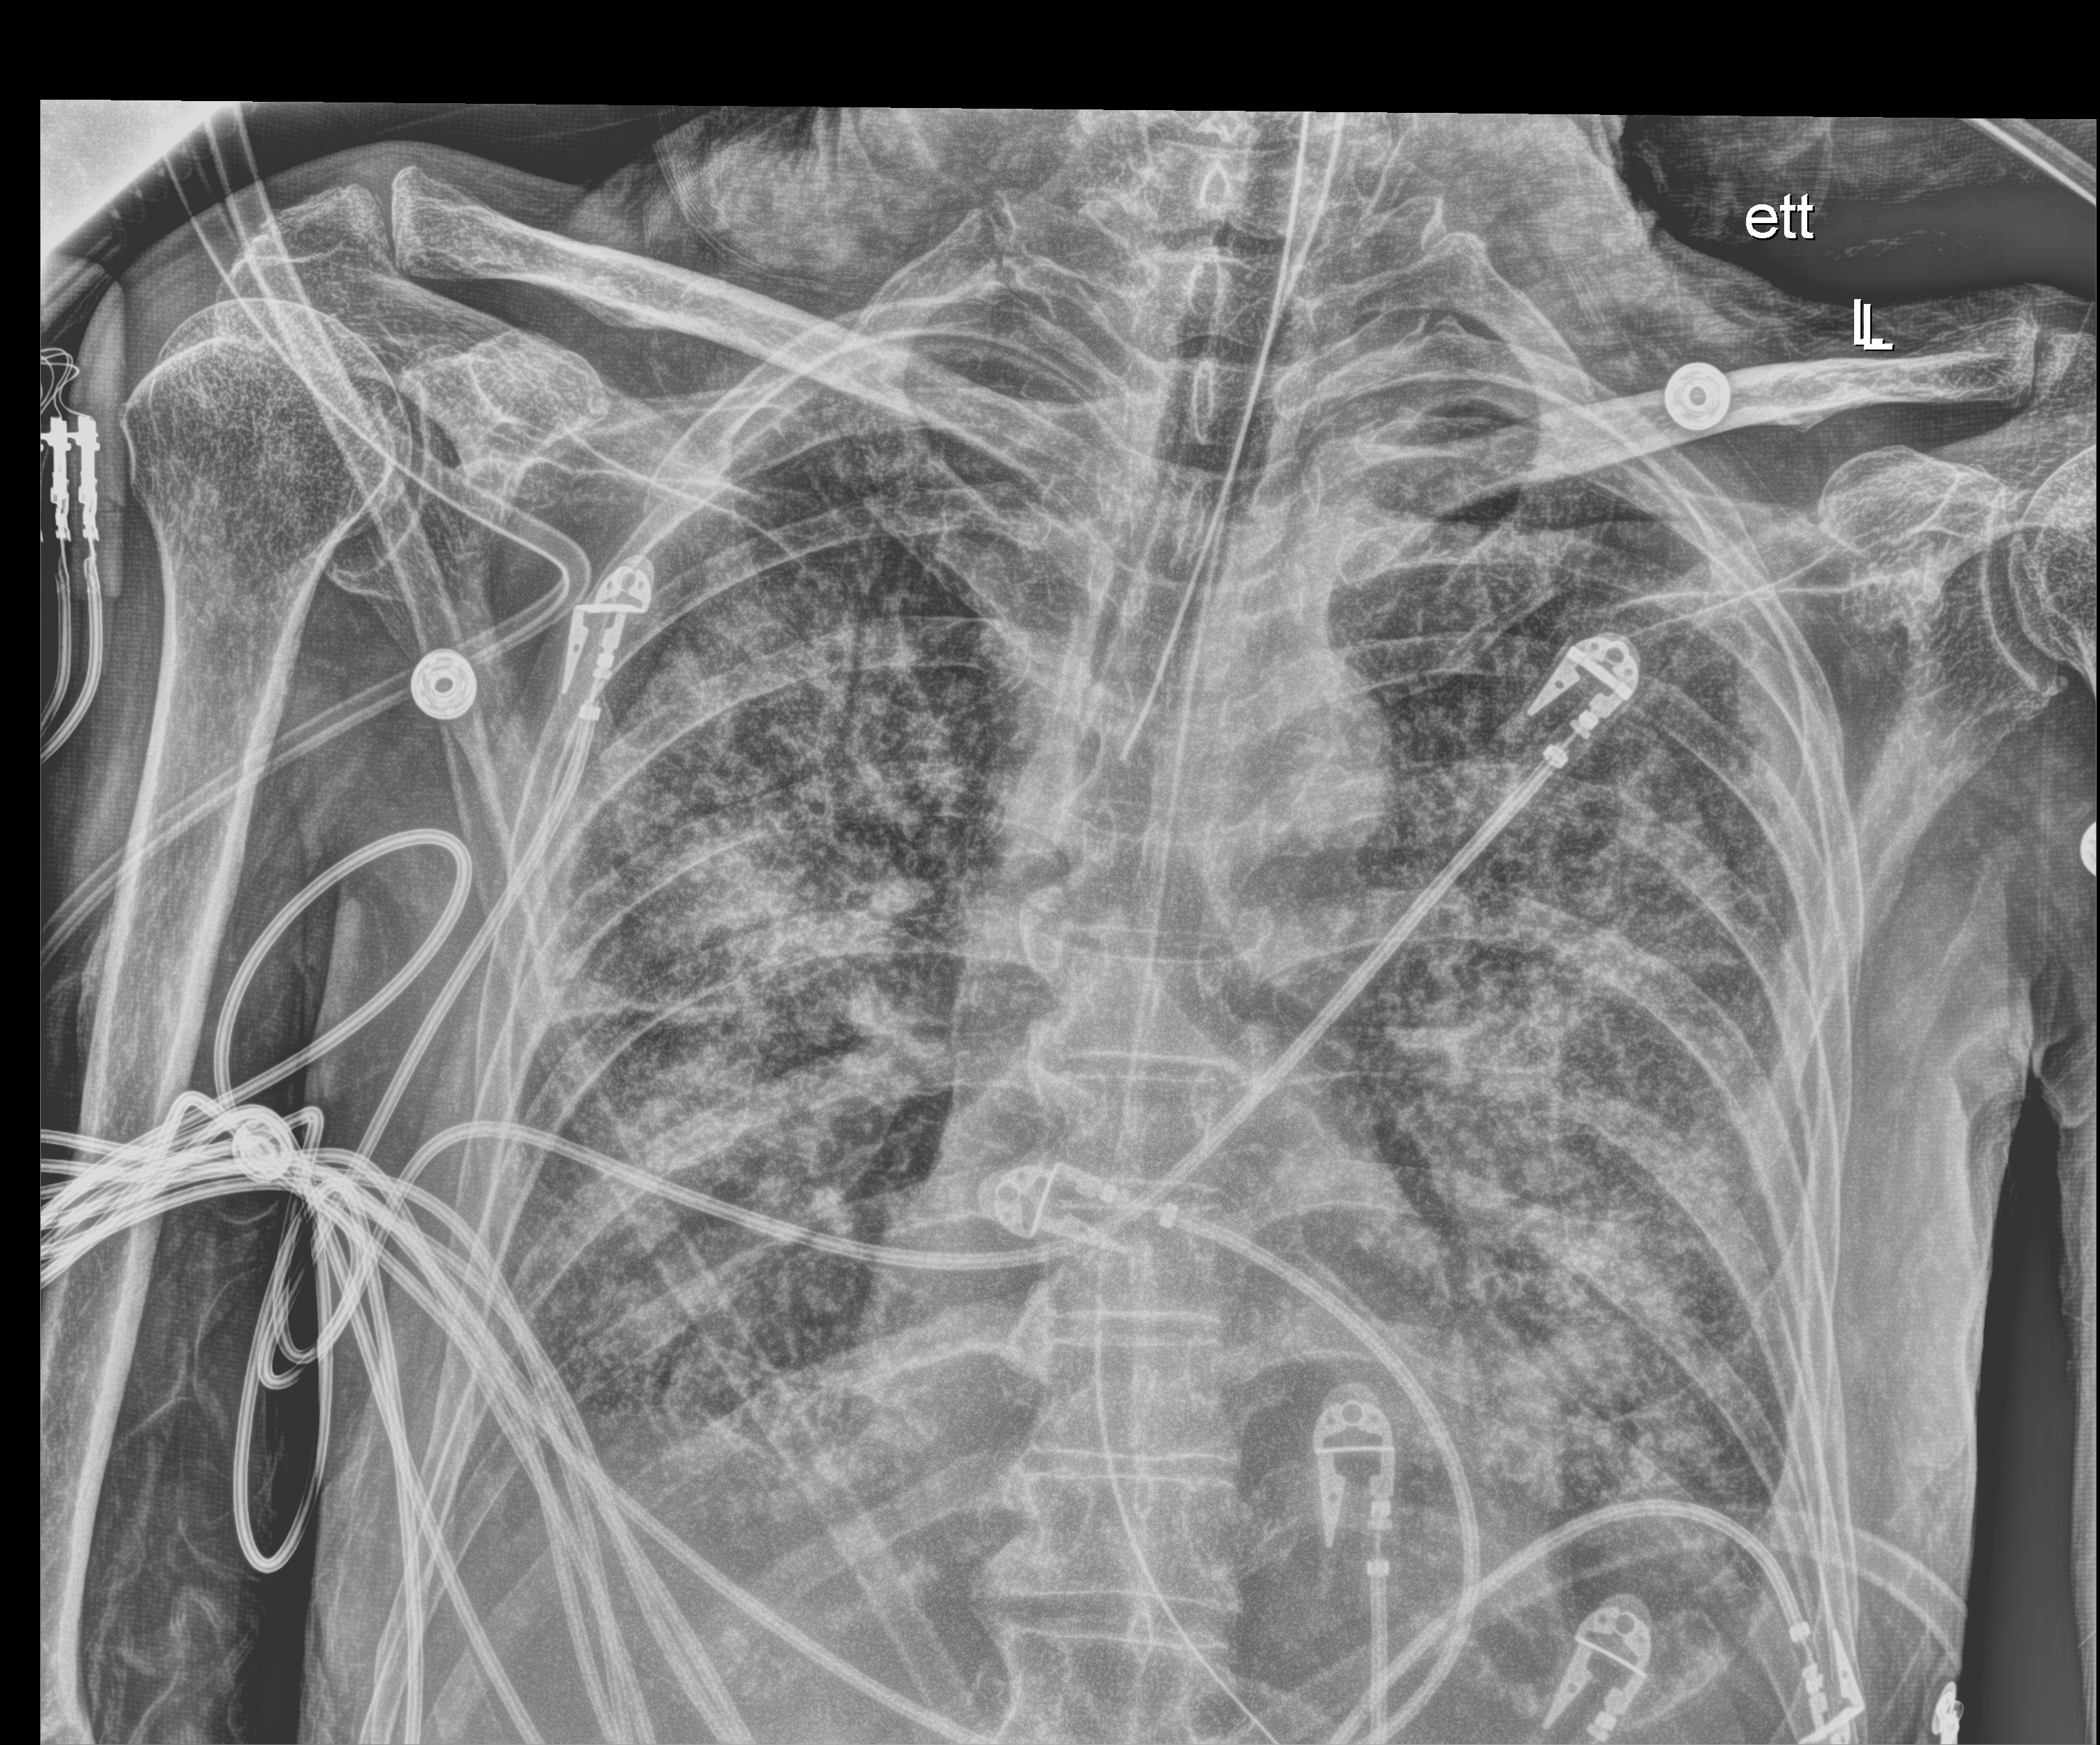
Bedside chest radiograph (digital radiography), anteroposterior (AP) projection. Male patient hospitalised with COVID-19, age 60–74 years.
Hospital-stay facts (about this admission, not read from this image; timing relative to this image not recorded): length of hospital stay: 42 days.